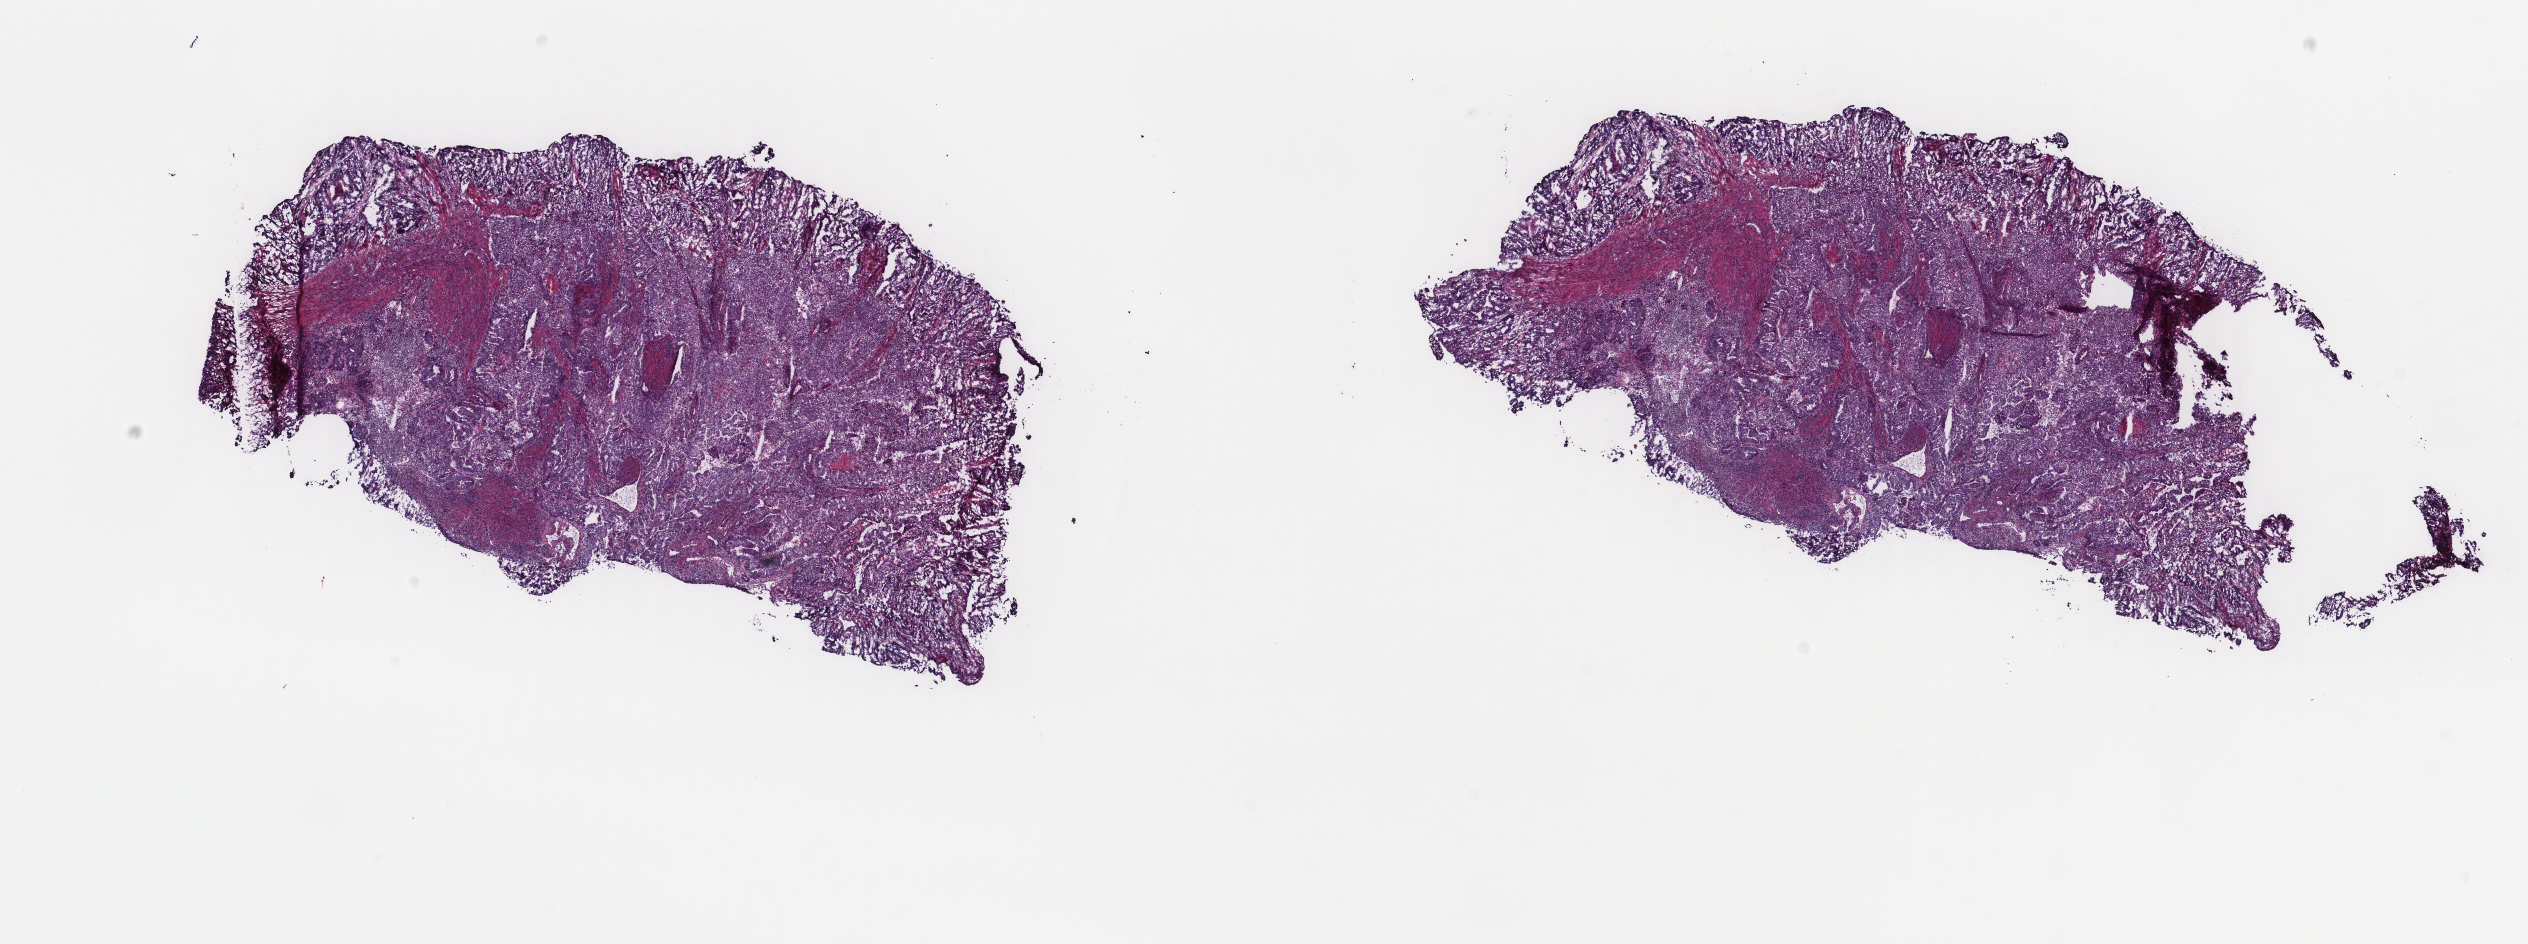
Digitized Hematoxylin and eosin (H&E) stained tissue section (whole slide) — shown as a low-resolution overview of the whole scanned area (about 20.1 x 7.5 mm, acquisition: 40x scan); frozen section from the top of the tissue portion; sample: primary tumour, uterus. Patient: female, age at initial diagnosis 74 years. Histologic grade: G3 (poorly differentiated). Slide review estimates, as recorded: tumour cells 80%, tumour nuclei 80%, normal cells 0%, stromal cells 15%, necrosis 5%. Inflammatory infiltration, as recorded: lymphocyte infiltration 30%, monocyte infiltration 30%, neutrophil infiltration 30%.
FIGO stage: IB. Pathologic diagnosis: Endometrioid adenocarcinoma, NOS (endometrium). Lymph nodes positive (case pathology): 0 of 12 examined.